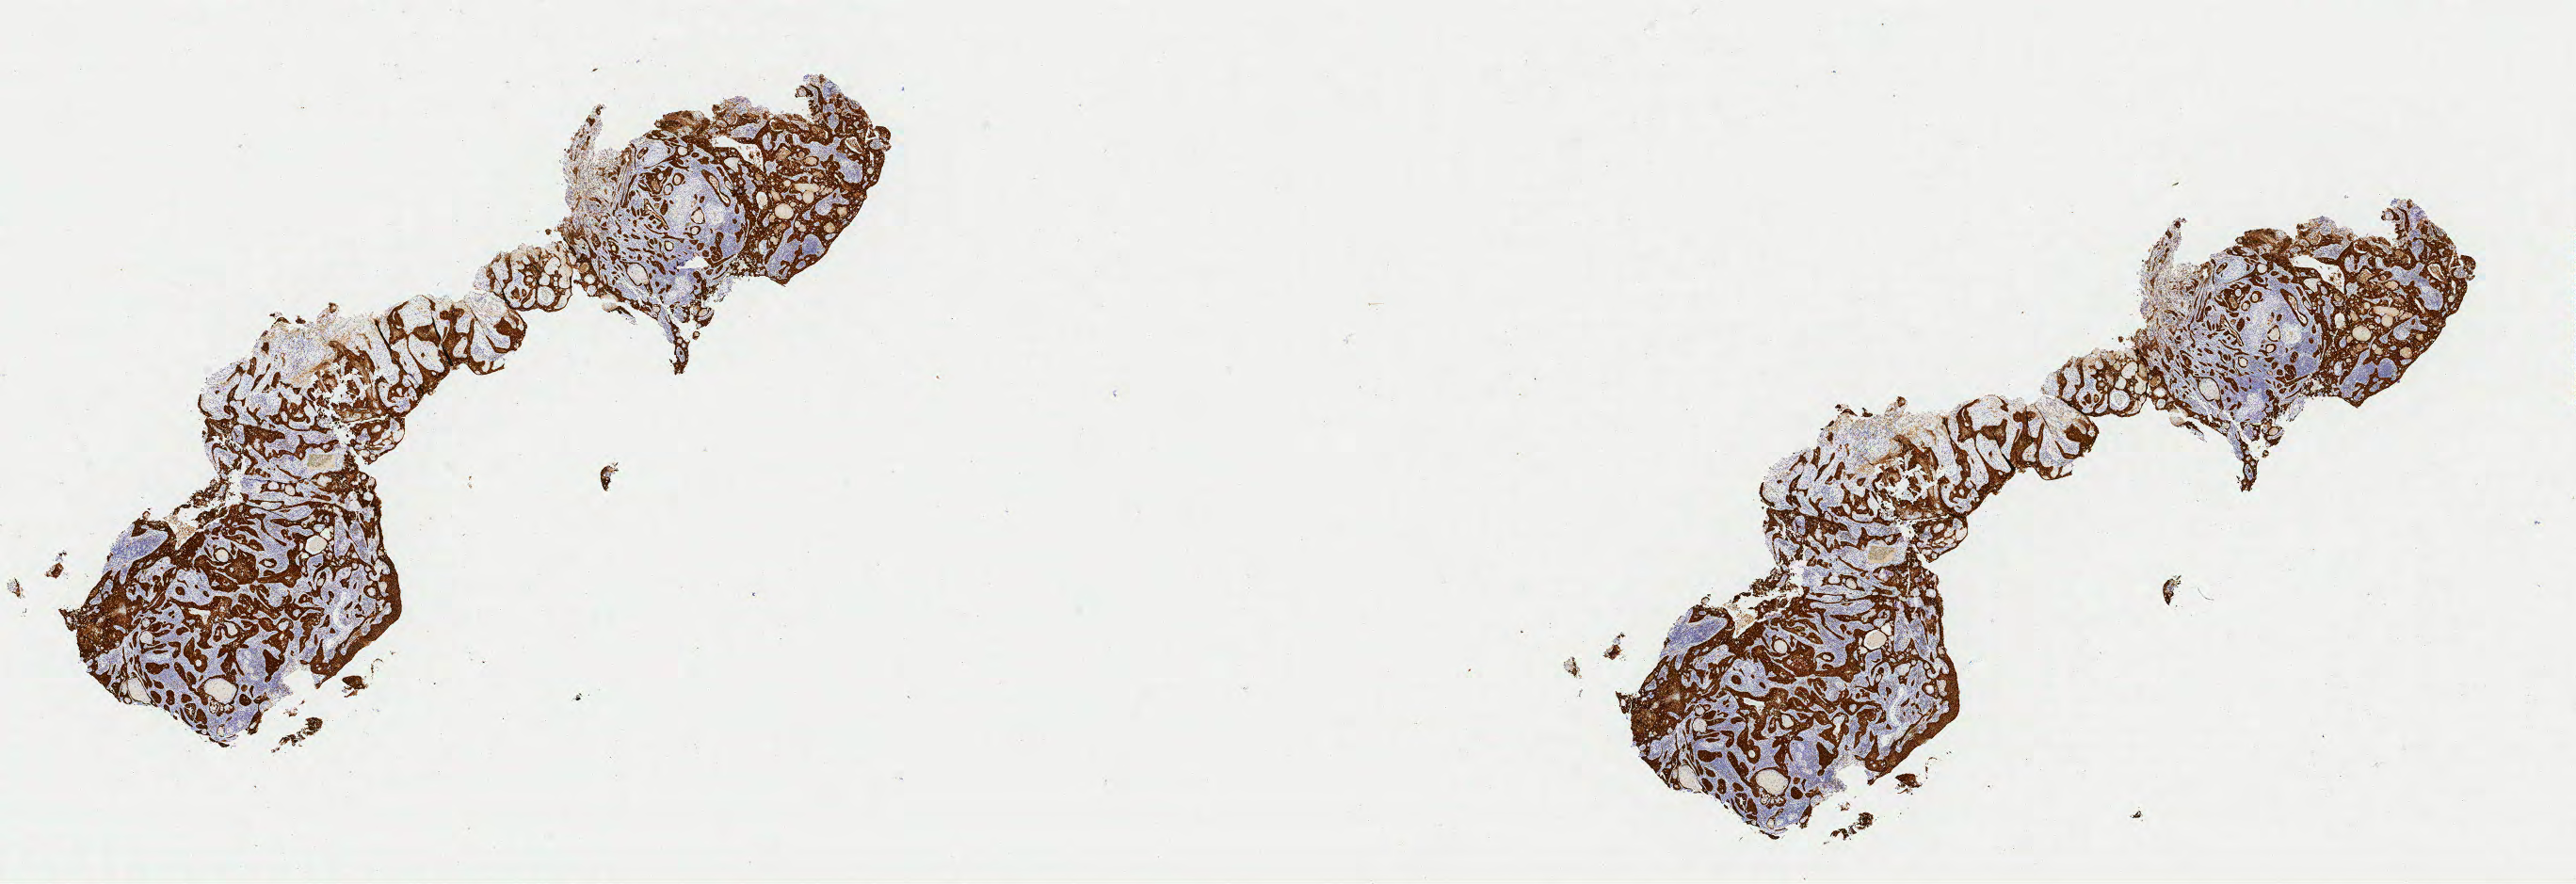
Whole-slide image, immunohistochemical stain for p16 (p16INK4a) — low-resolution overview of the scanned area, about 21.7 x 7.5 mm. Specimen: tumor tissue. Site: cervix. Female patient, age 60 years.
Diagnosis: Squamous cell carcinoma, keratinizing, NOS.